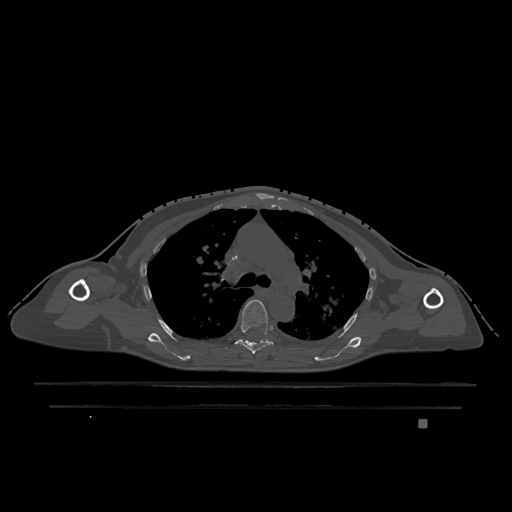
CT including the spine, one axial slice; position 836 of 1317 along the scan axis; bone window (W 1800 / L 400 HU); 512 × 512 image matrix, field of view 500 × 500 mm. Female patient, age 74 years. Case-level facts recorded for this patient, not image findings: primary cancer: lung; vertebrae with lytic lesions (as recorded): T1, T4, T5, T6, L4, L5.
Structures marked on this image (semi-automatically segmented with operator editing):
- T5 vertebra: box from (x=227, y=300) to (x=273, y=354) px